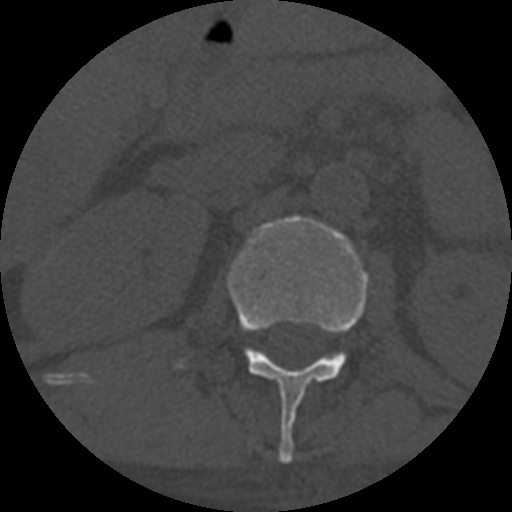
CT including the spine, one axial slice; slice 284 of 708 in the series (ordered by position); reconstruction kernel STANDARD; 120 kVp; one of 3 acquisitions stored at this slice position; bone window (W 1800 / L 400 HU); 1.25 mm slice thickness; 512 × 512 image matrix, field of view 160 × 160 mm. Patient age 55 years. From the clinical record (not read from this slice): primary cancer: colon.
Annotated regions visible in this slice (semi-automatic segmentation, software-assisted and operator-edited):
- L1 vertebra: bounding box [x1, y1, x2, y2] px = [176, 216, 368, 464]